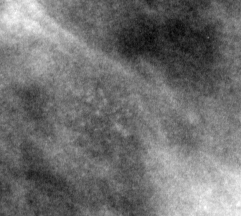
Region of interest cut from a scanned film mammogram (one marked finding), right breast, MLO view.
Finding: calcifications, morphology pleomorphic, distribution clustered; BI-RADS assessment category 4; subtlety rating 1 on a 1 (subtle) to 5 (obvious) scale; pathology (as recorded): malignant.